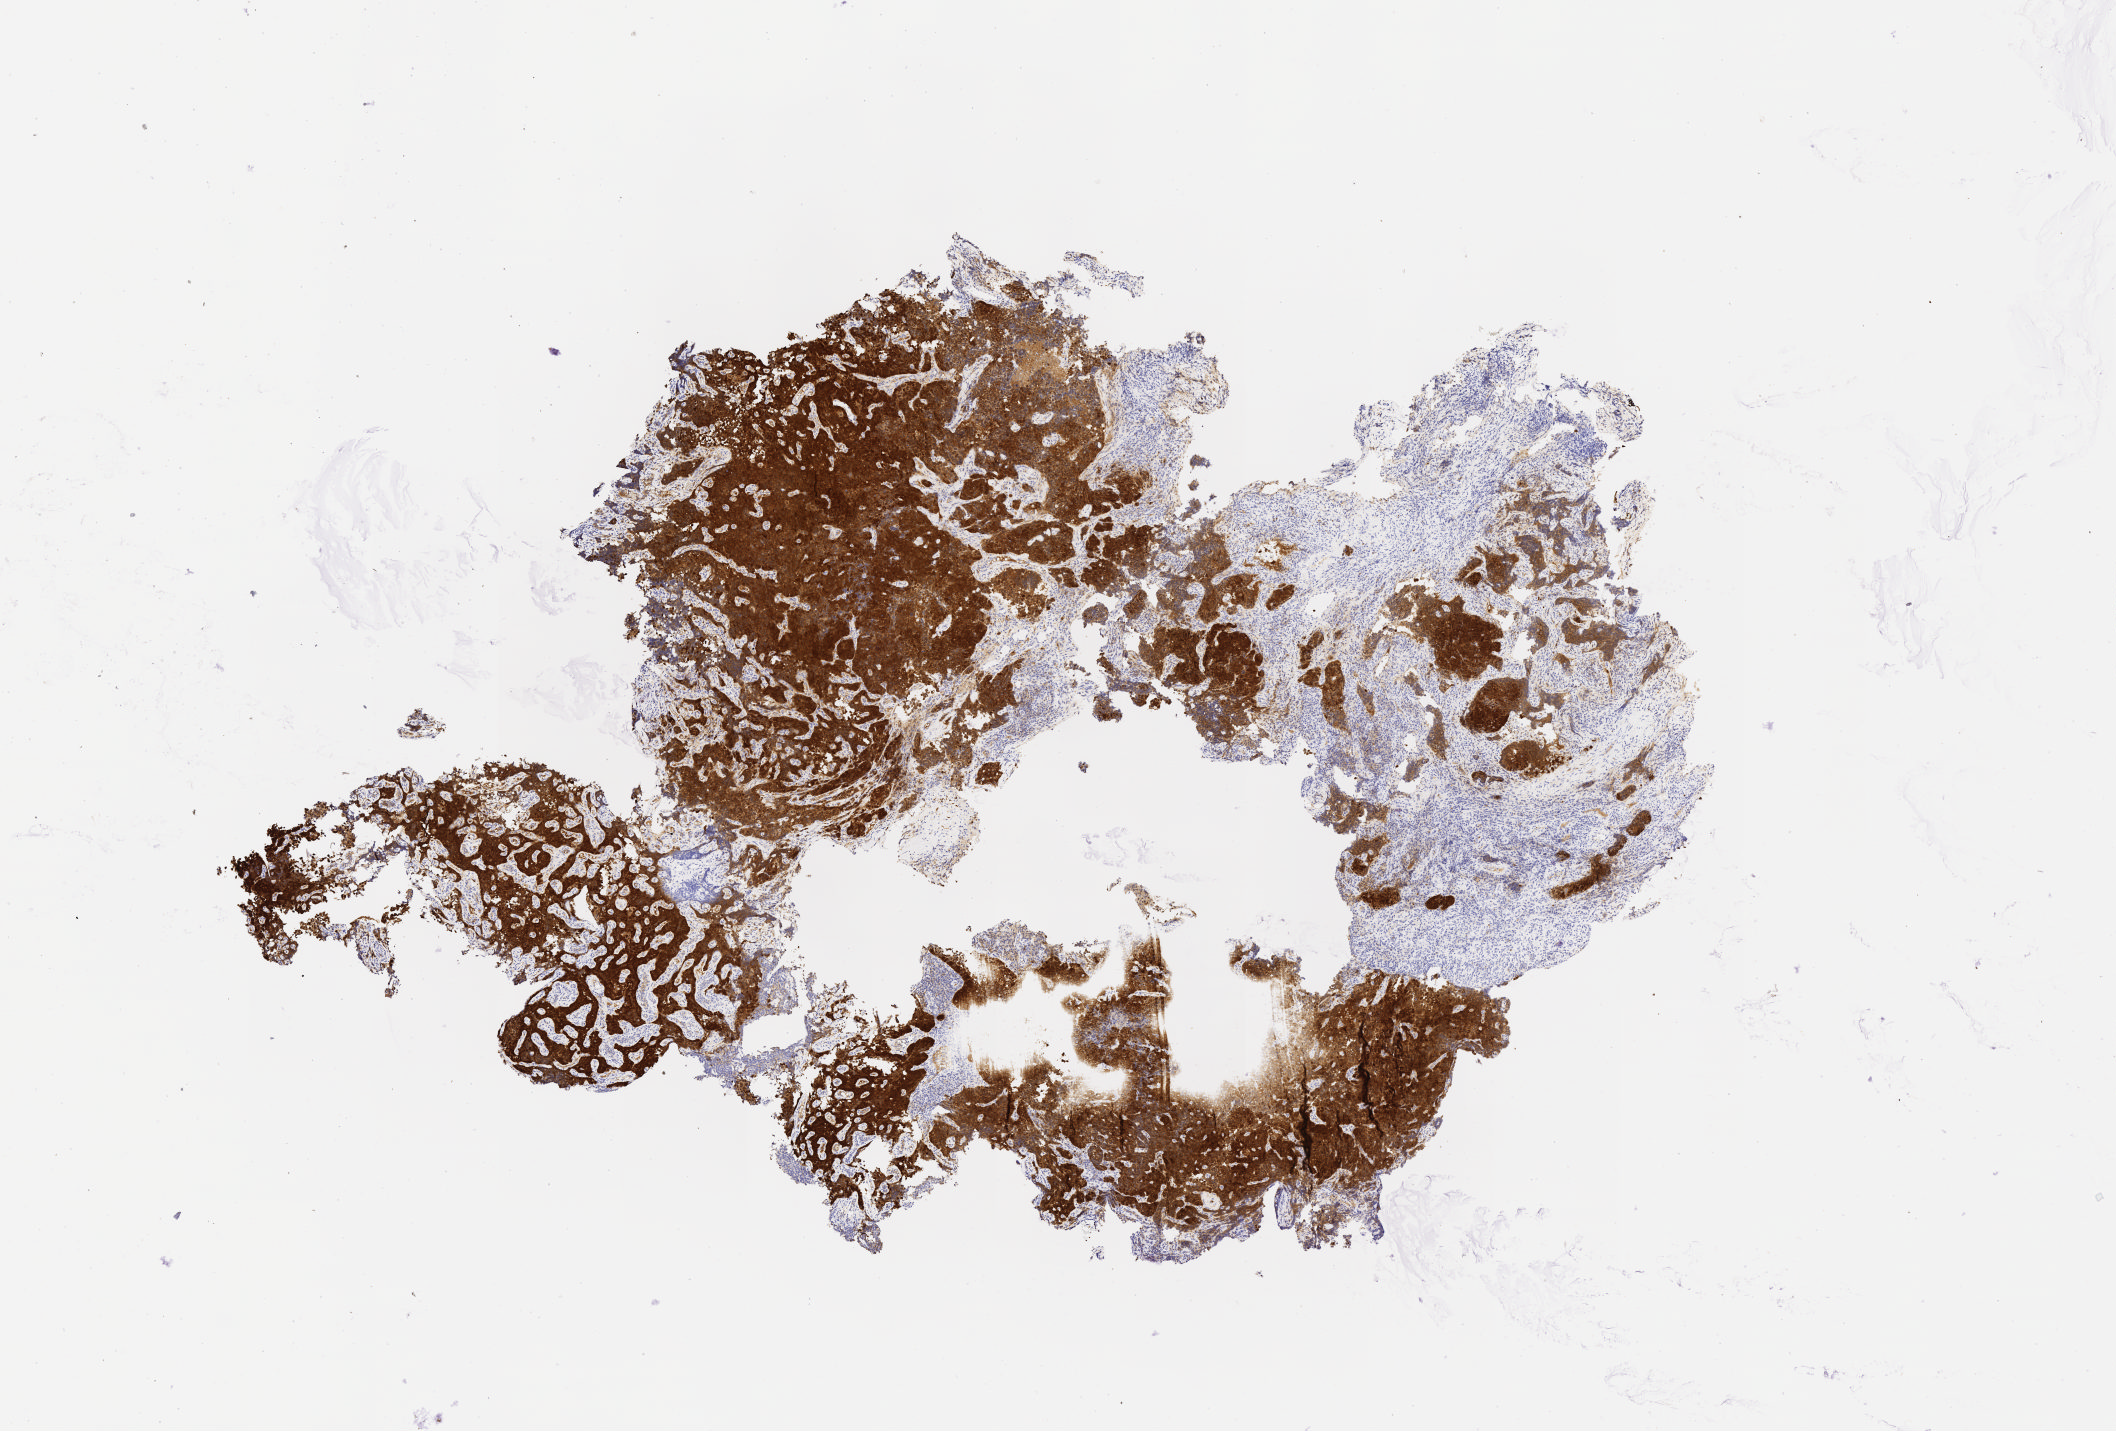
IHC for p16 (p16INK4a), whole-slide image, low-resolution overview of the scanned area, about 8.6 x 5.8 mm. Specimen: tumor tissue. Site: cervix. Patient female; aged 72.
- diagnosis: Squamous cell carcinoma, large cell, nonkeratinizing, NOS